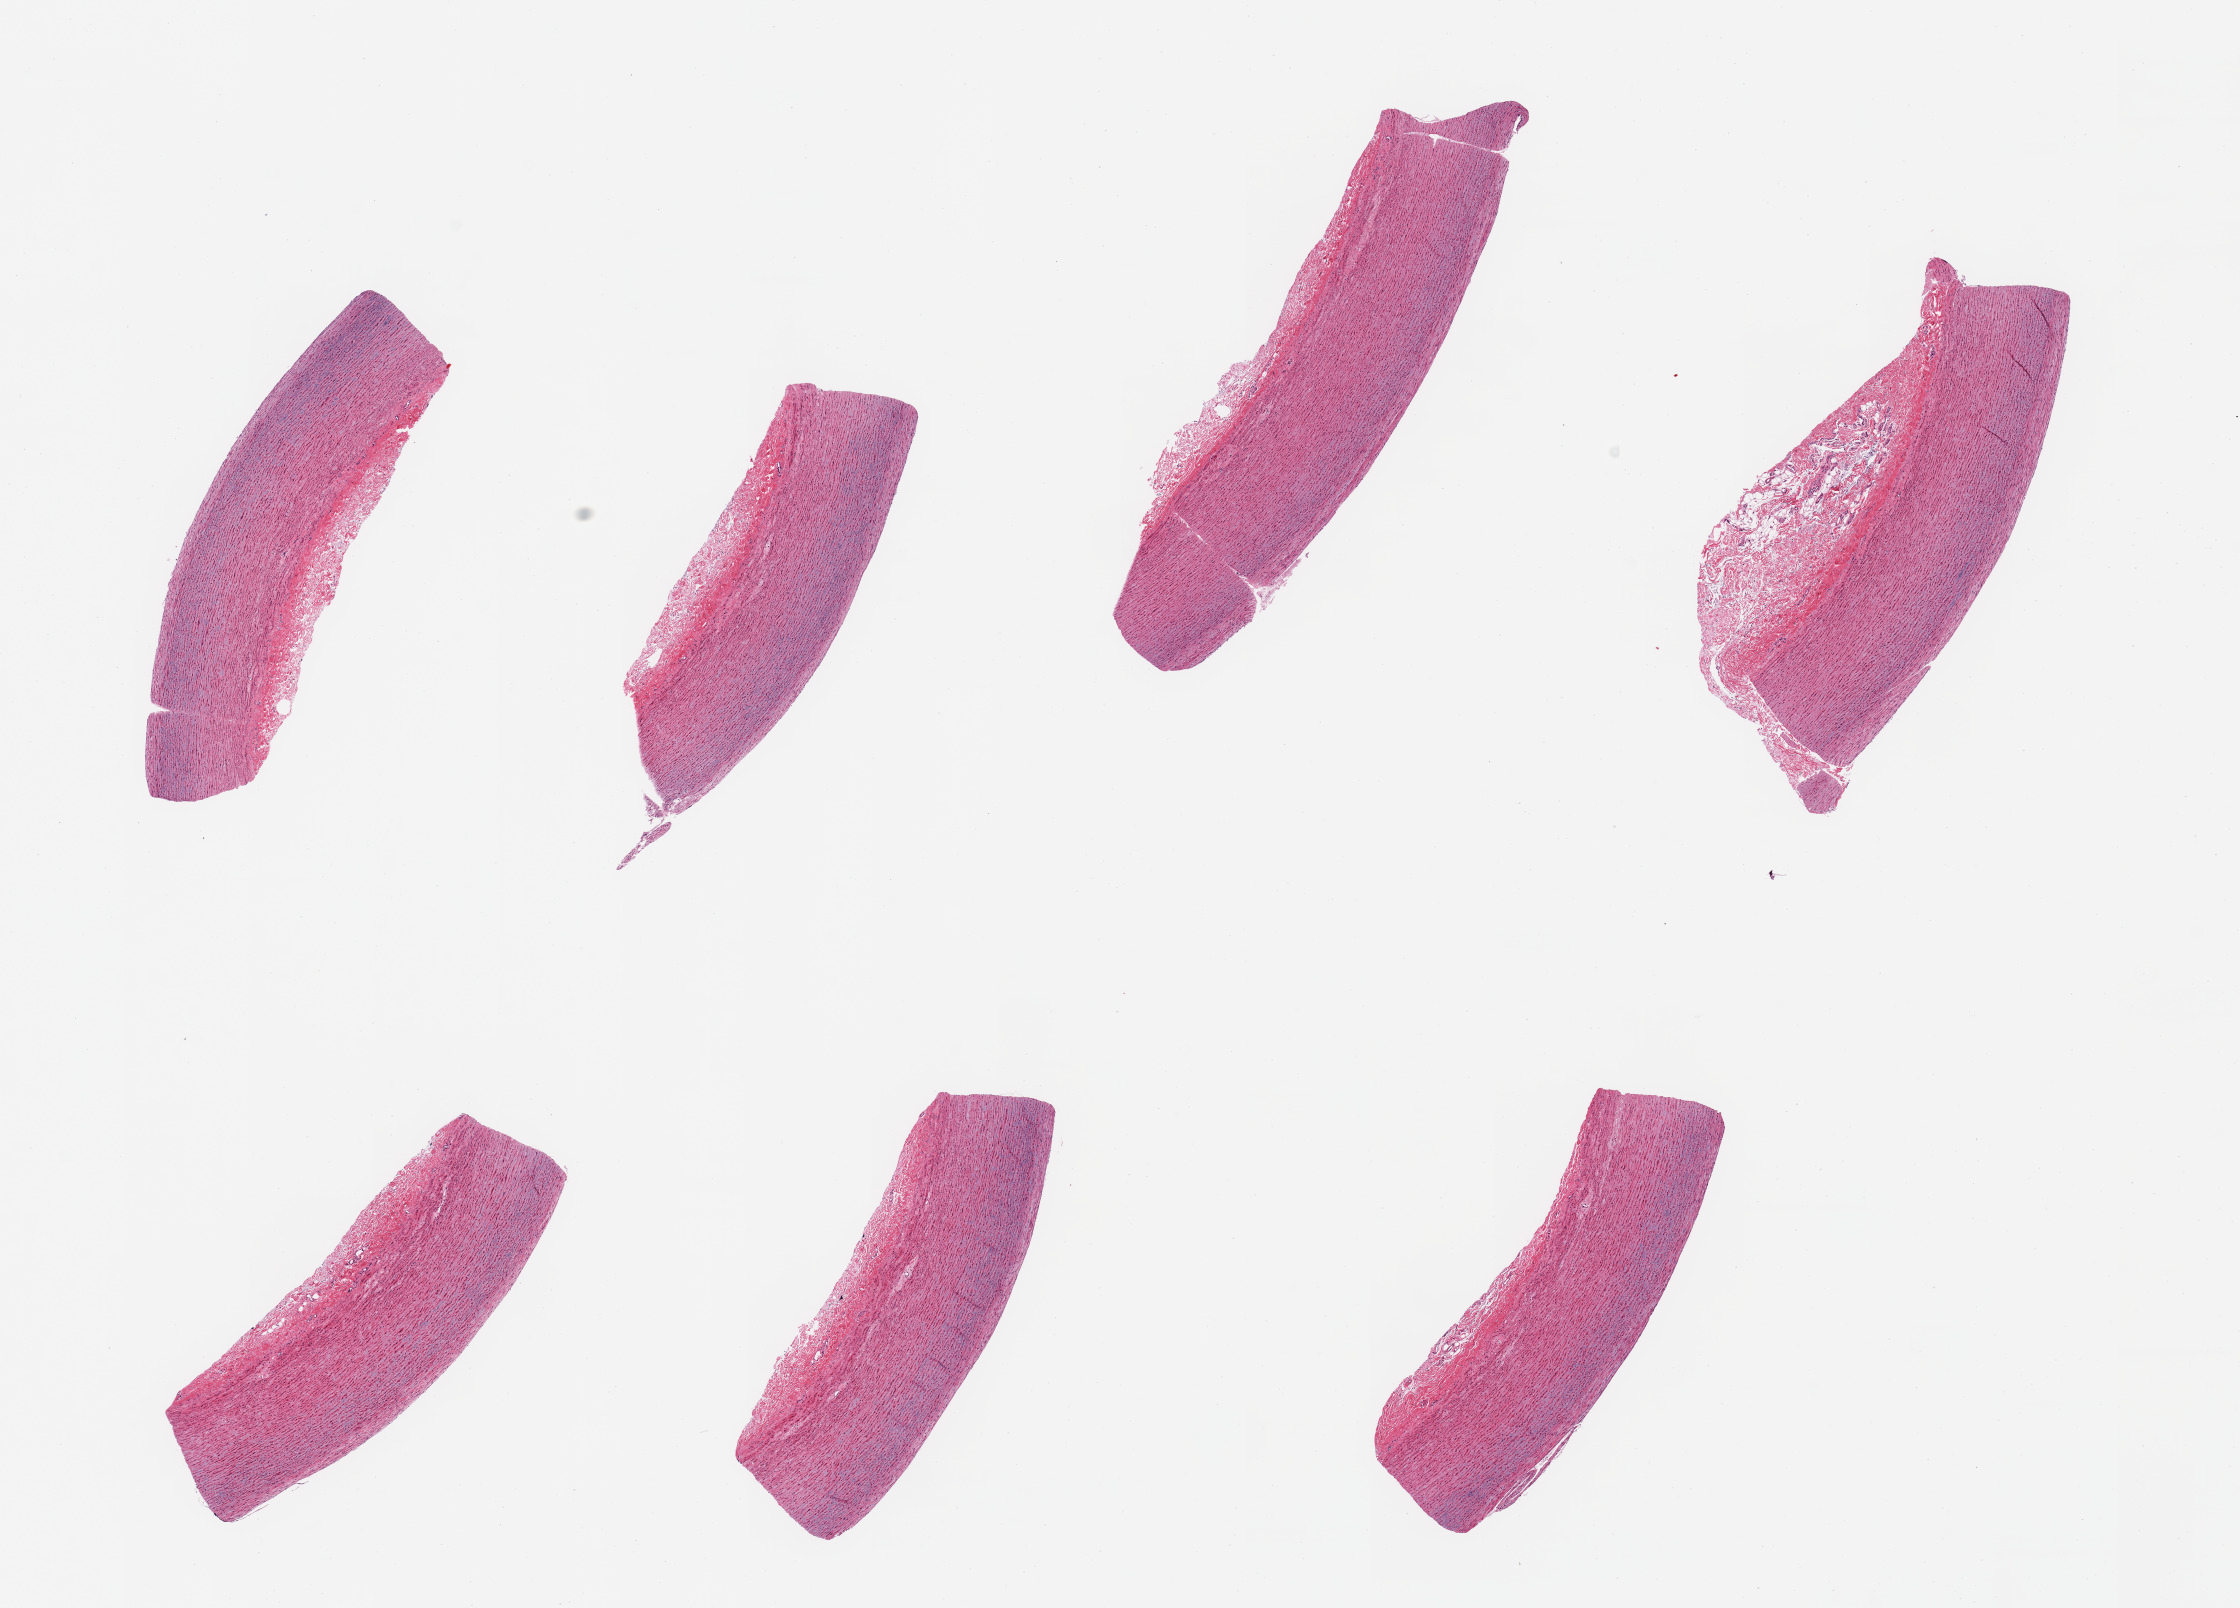
Whole-slide image, haematoxylin and eosin stain — whole scanned area (about 17.7 x 12.7 mm, acquisition: 20x scan) shown as a low-resolution overview. PAXgene-fixed, paraffin-embedded tissue. Target tissue: aorta. Tissue donor sample.
Pathologist's review note for this sample: 6 pieces, trace atherosis.